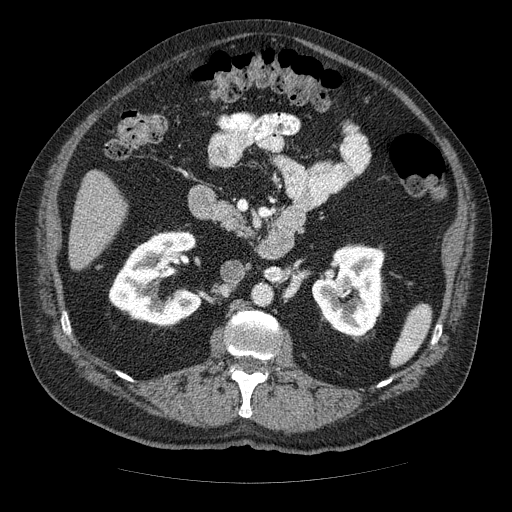
Contrast-enhanced abdominal CT (liver protocol), one axial slice; position 13 of 85 along the scan axis; reconstruction kernel STANDARD; 120 kVp; soft-tissue window (W 400 / L 40 HU); 2.5 mm slice thickness; 512 × 512 image matrix, field of view 420 × 420 mm. From the clinical record (not read from this slice): diagnosis: hepatocellular carcinoma (patient treated with transarterial chemoembolisation; whether this scan precedes or follows treatment is not stated here); TNM stage (as recorded): Stage-IIIA; Child-Pugh class: A; tumour nodularity: multinodular.
Annotated regions visible in this slice (semi-automatic segmentation, software-assisted and operator-edited):
- liver parenchyma outside the tumour (the mass and vessels are separate outlines, so this box may not span the whole liver): bounding box <68,170,126,268> (left, top, right, bottom; pixels)